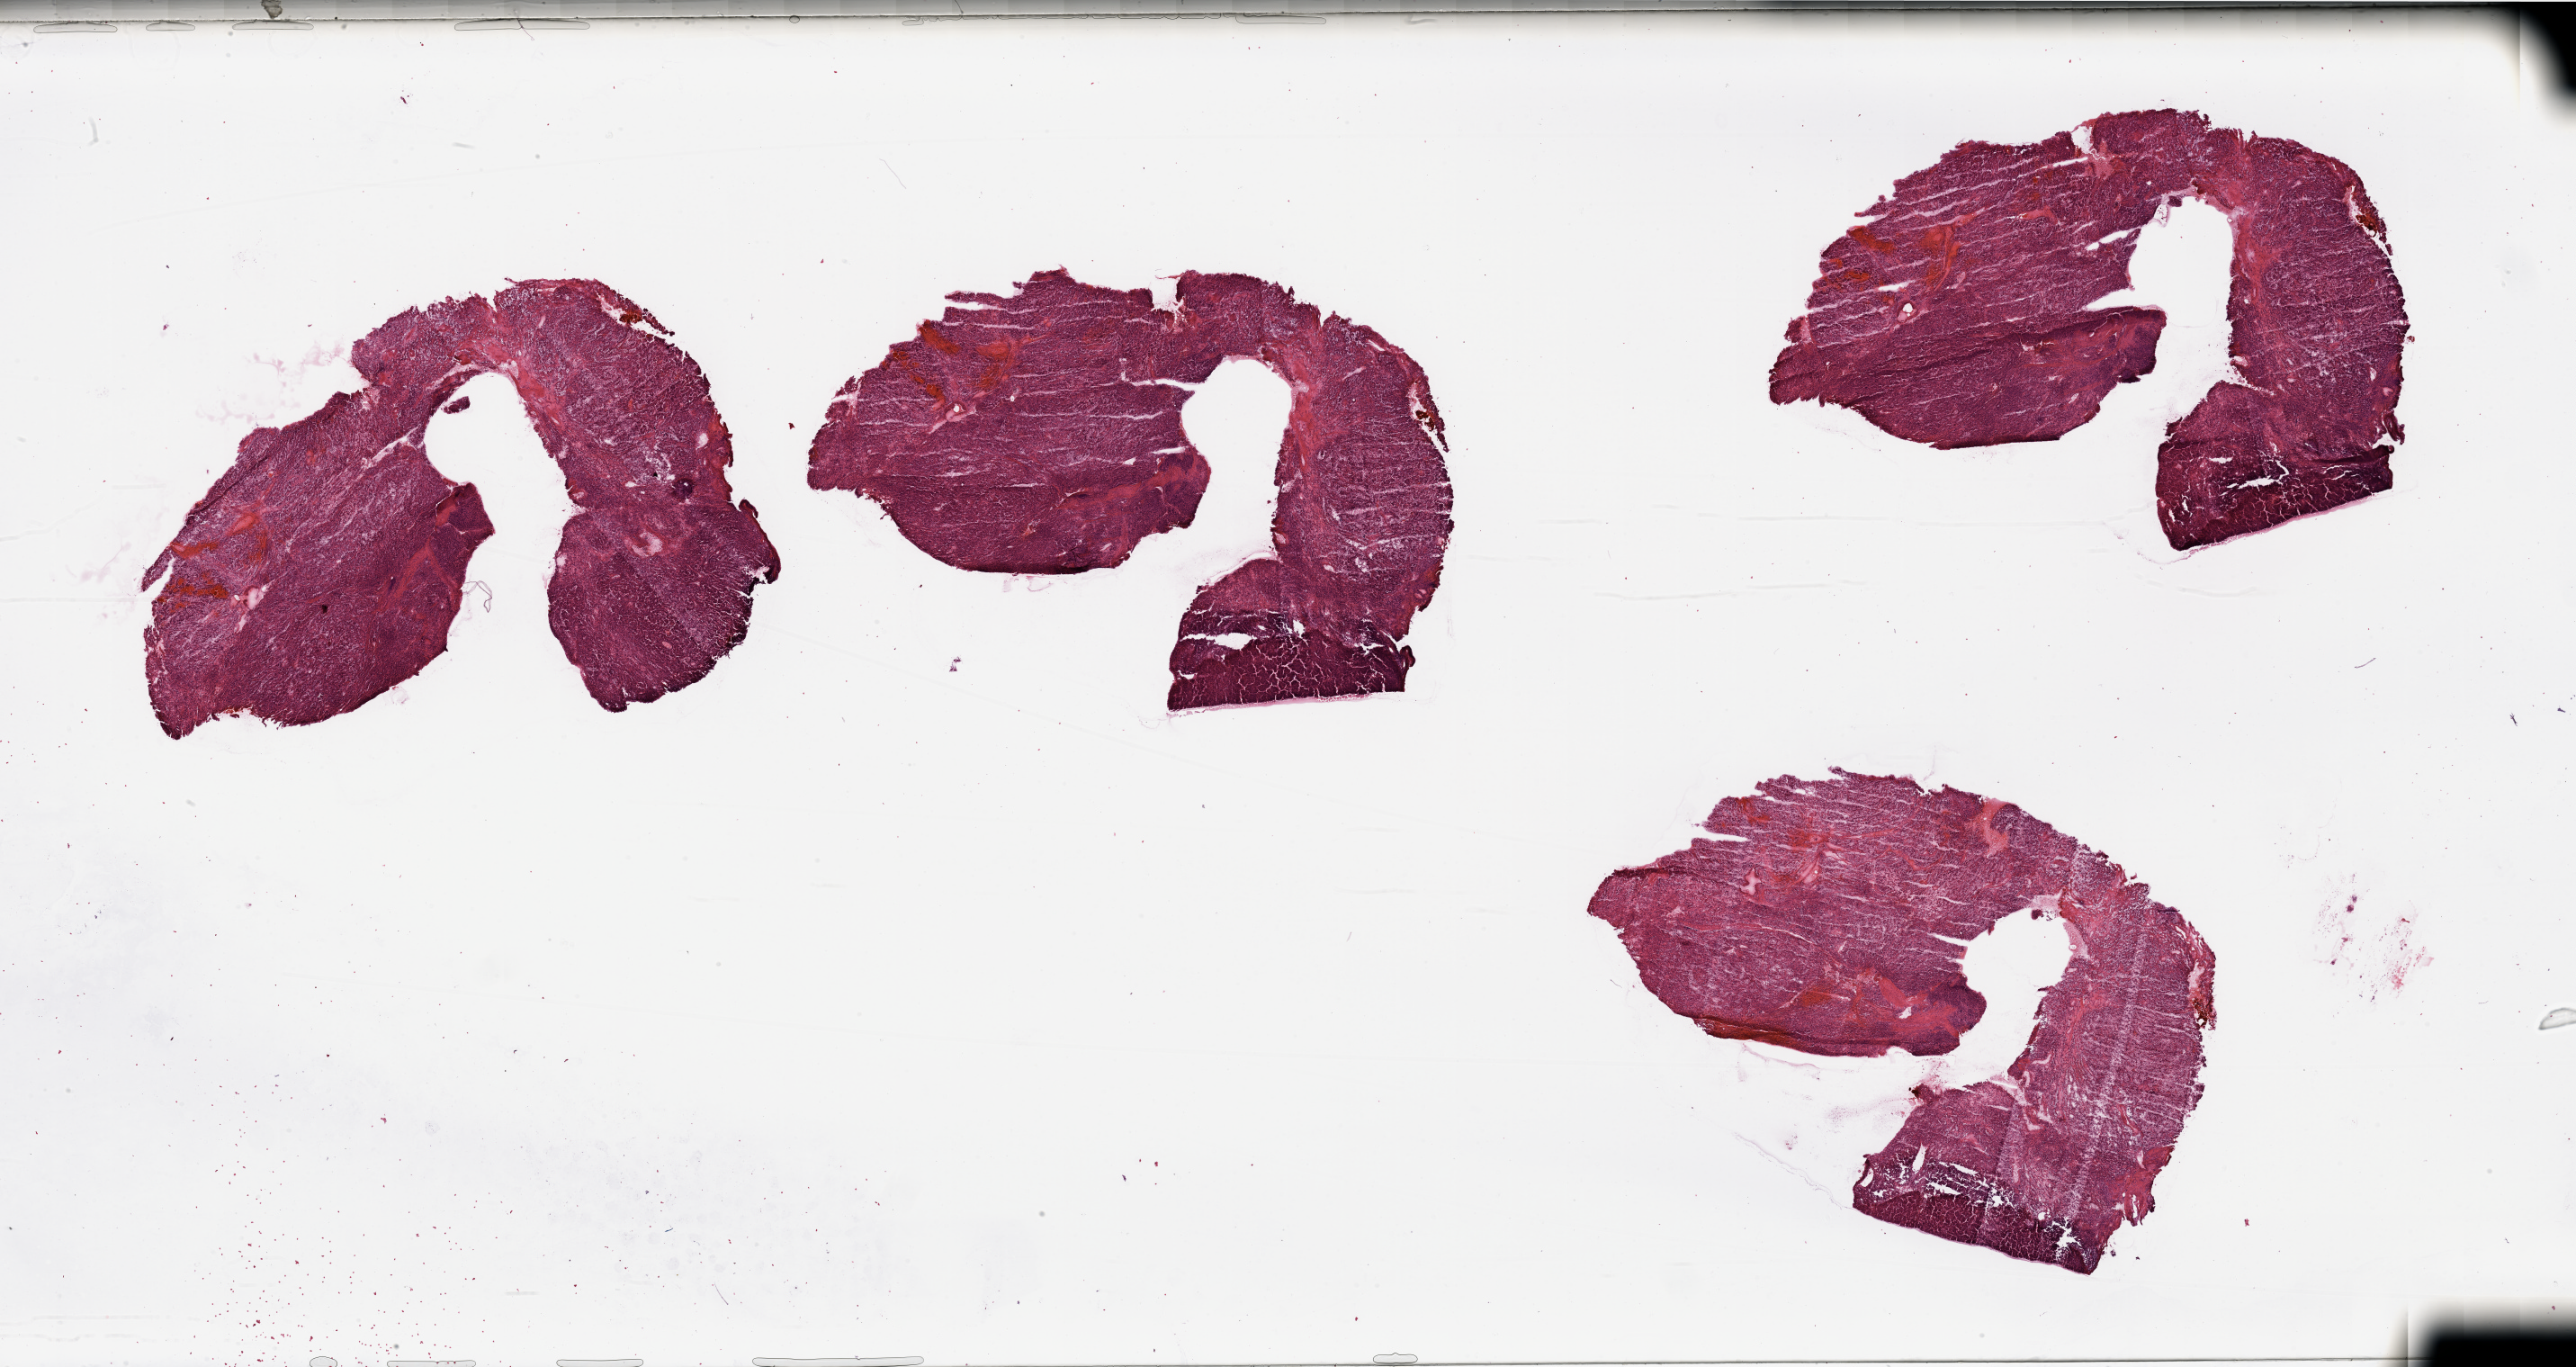
Whole-slide histology image, H&E-stained, whole scanned area (about 45.3 x 24.0 mm, from a 20x scan) shown as a low-resolution overview, tumour tissue sample, sampled site: kidney. Patient: male, age 78 years. Histologic grade: G2 (moderately differentiated). Slide review estimates, as recorded: tumour nuclei 85%, necrosis 5%.
• AJCC pathologic stage: I
• diagnosis: Renal cell carcinoma, NOS
• primary tumour site (as recorded): upper pole